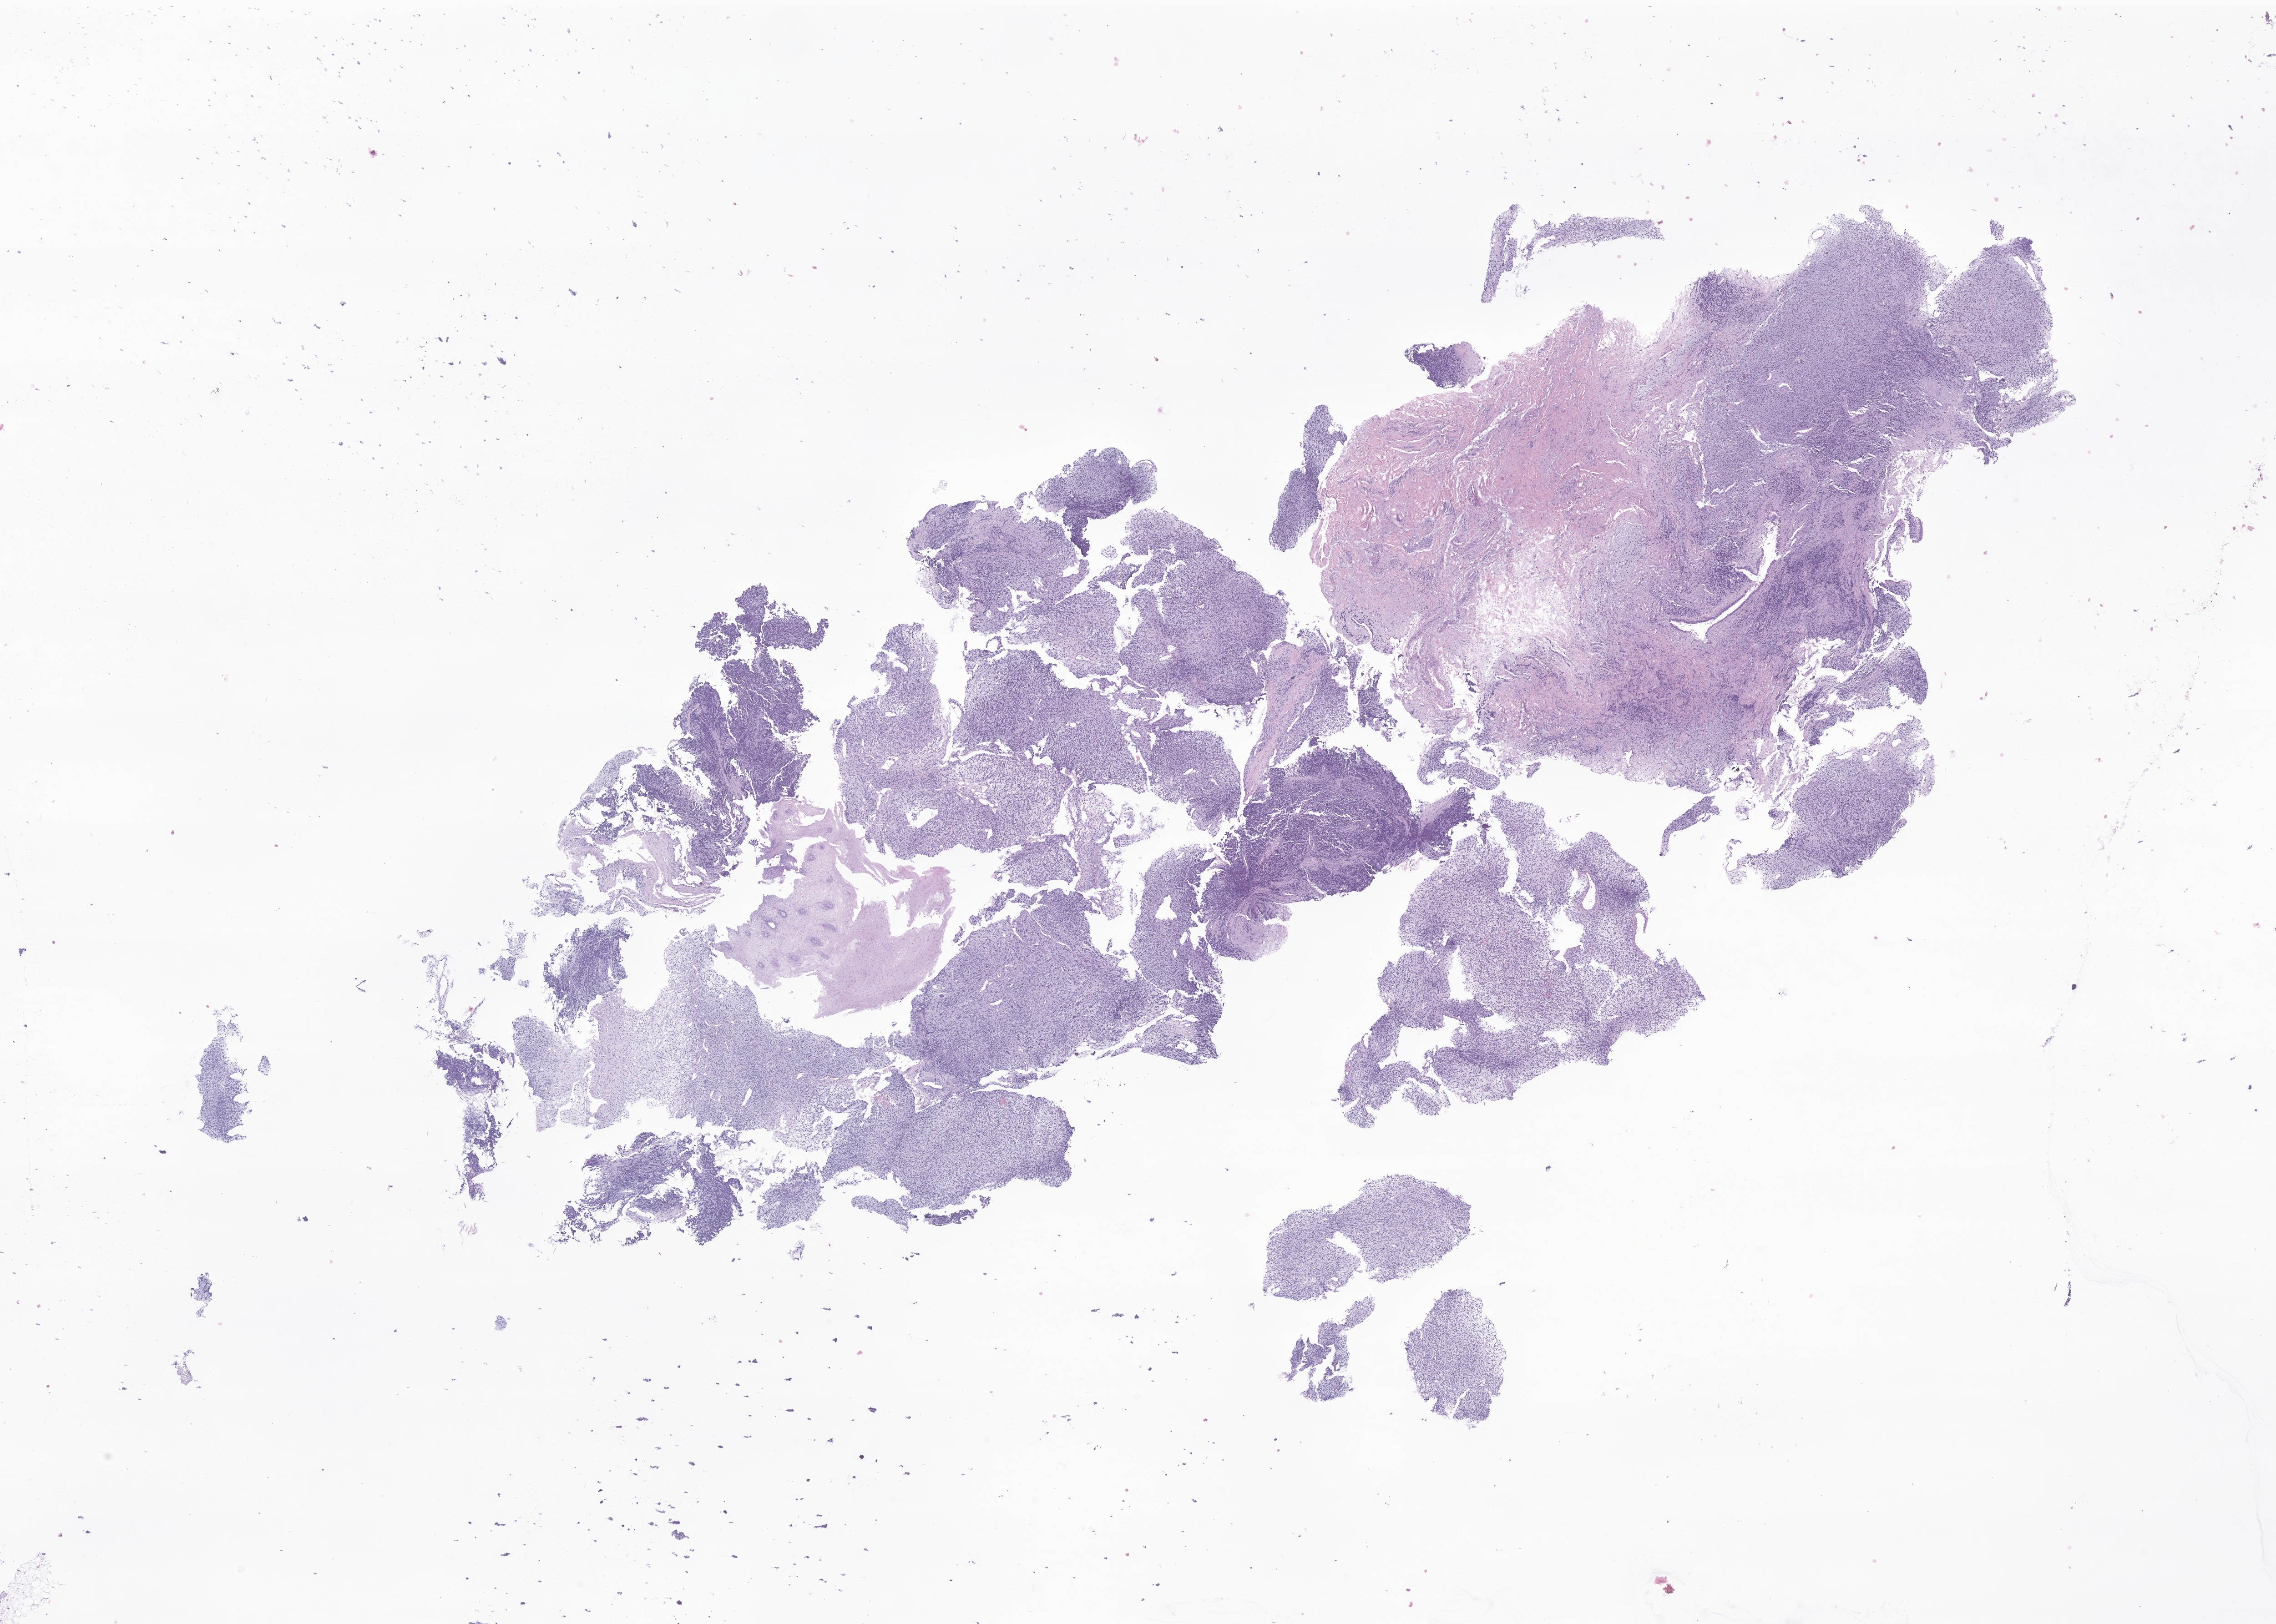
Hematoxylin and eosin (H&E) whole-slide image of tumor tissue from the soft tissues of head and neck — whole scanned area (about 21.1 x 15.1 mm) shown as a low-resolution overview, FFPE section. Male patient, age 158 months (13 years 2 months).
* diagnosis (ICD-O-3 morphology term): Embryonal rhabdomyosarcoma, NOS